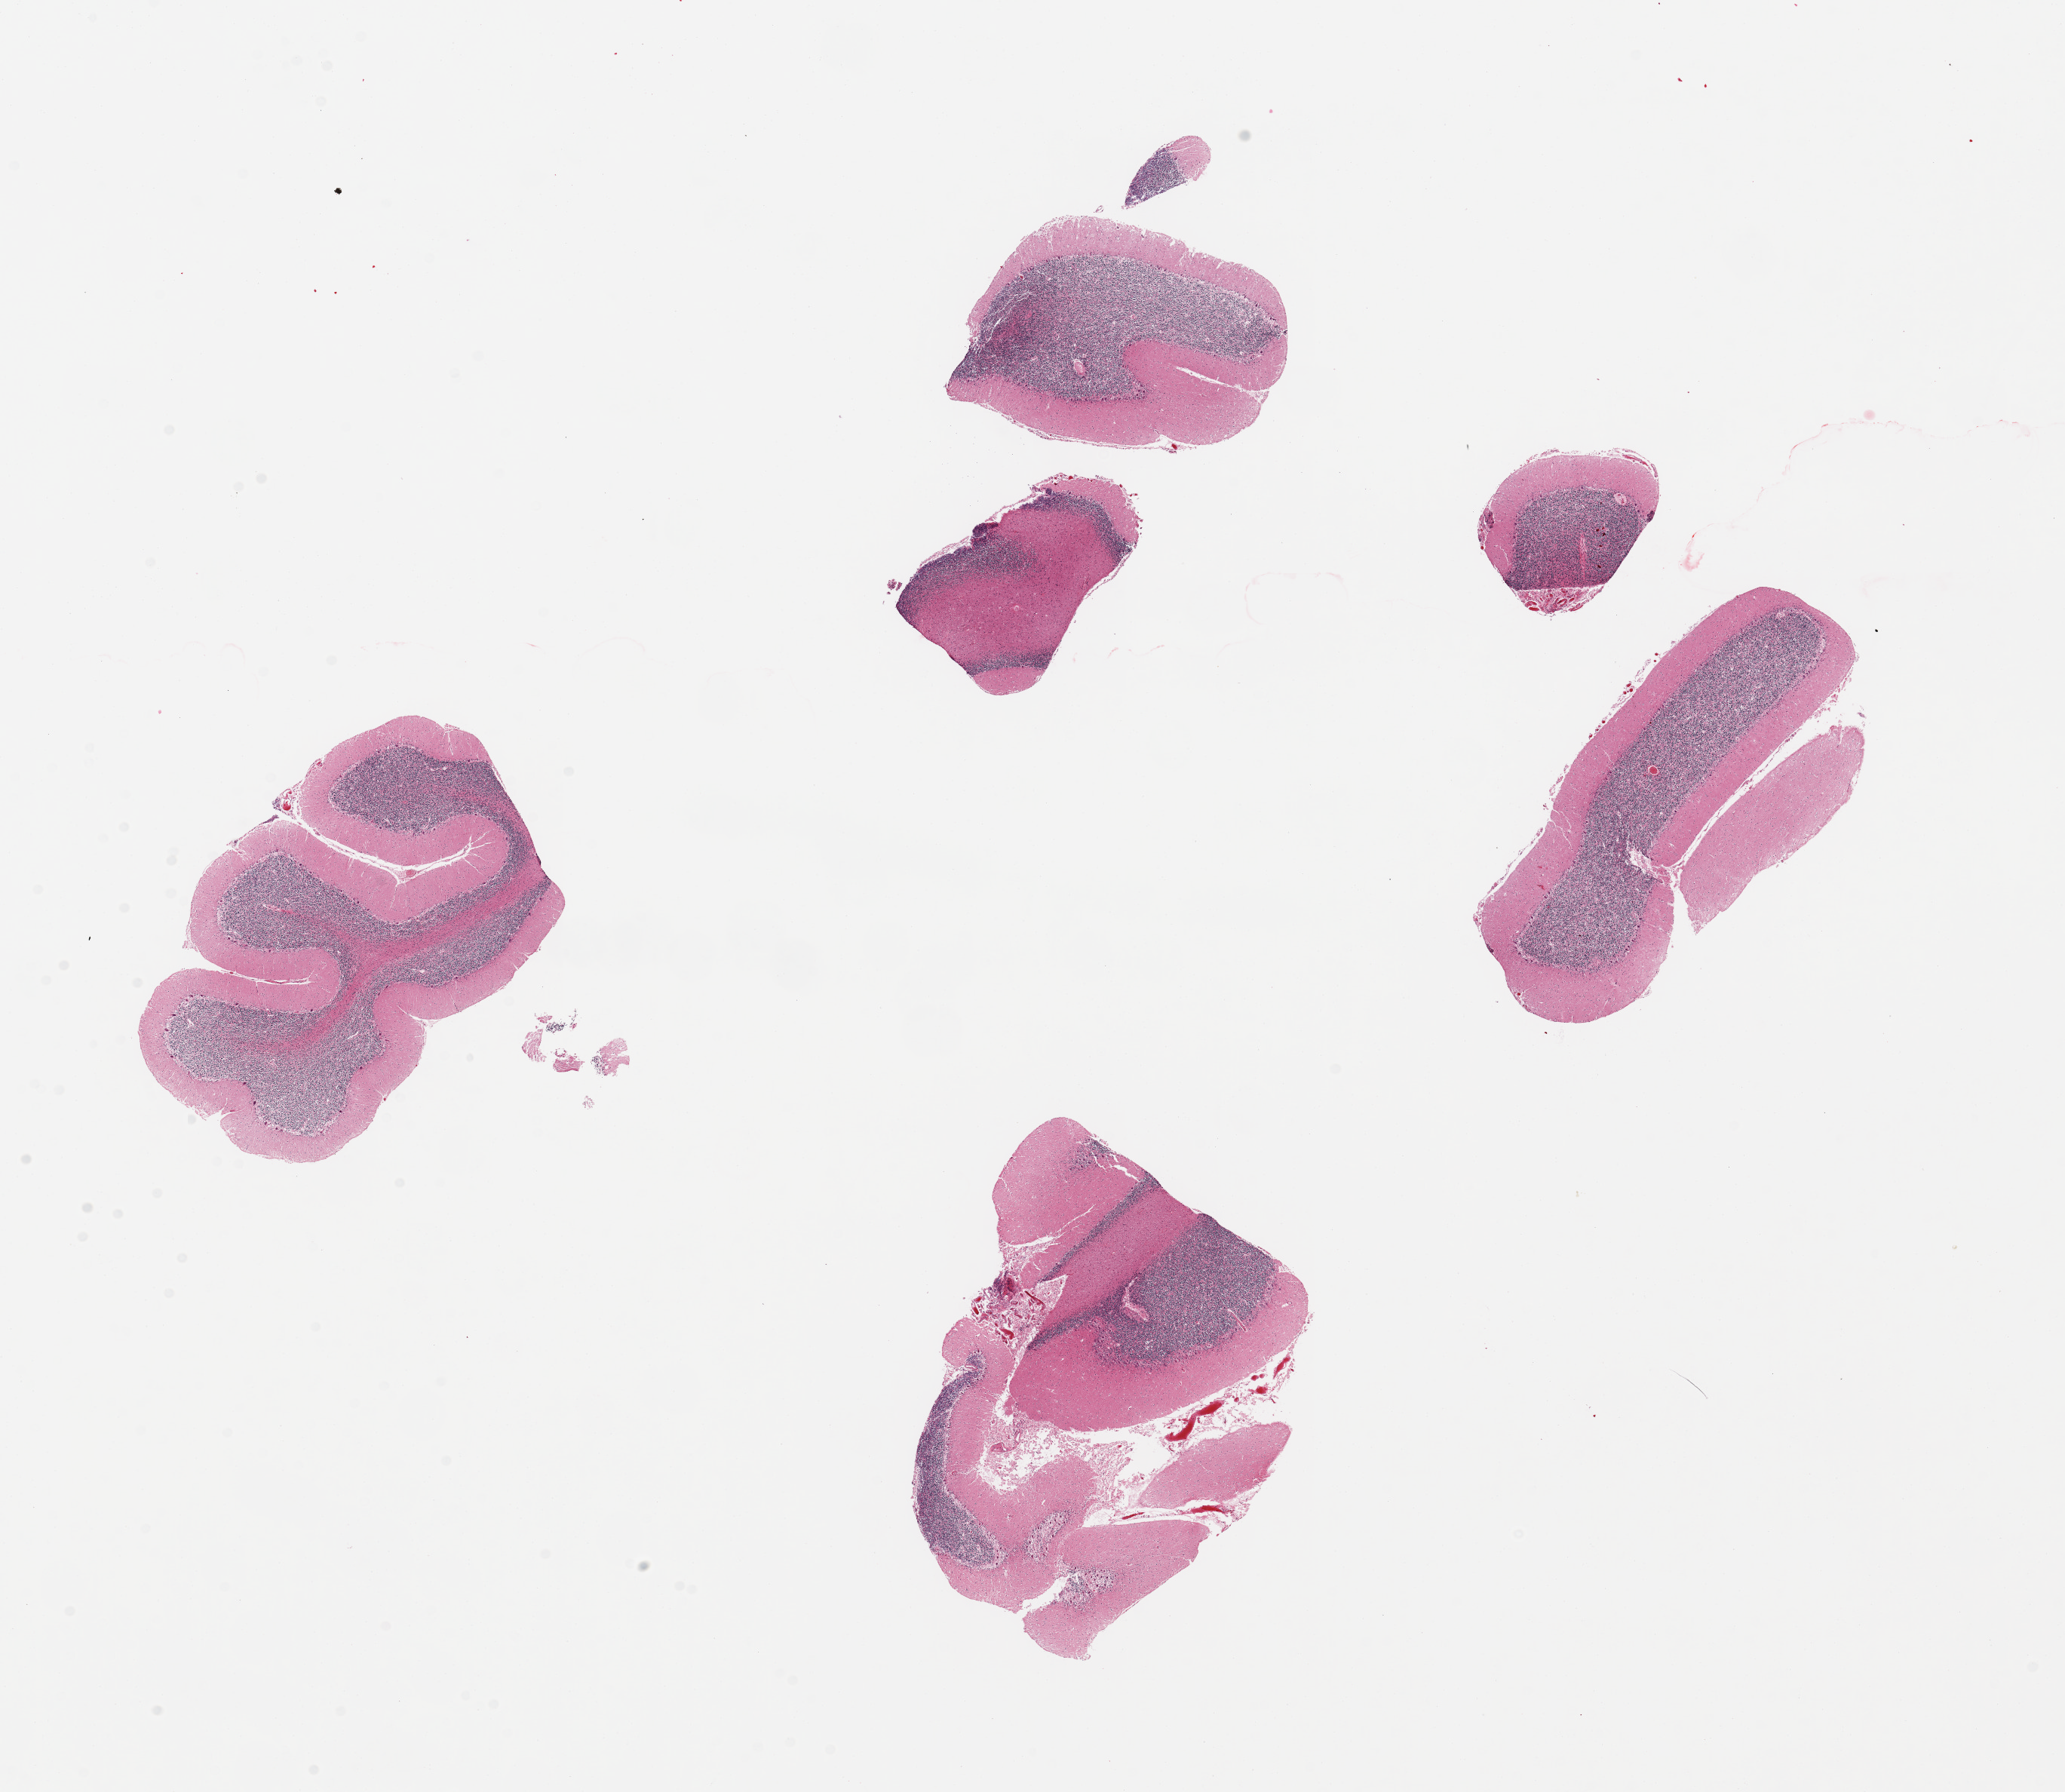
H&E whole-slide image, a low-resolution overview of the entire scanned area, about 21.7 x 18.8 mm. PAXgene-fixed, paraffin-embedded tissue. Target tissue: cerebellum. Tissue donor sample. Donor: female.
Pathologist's review note for this sample: 6-7 pieces (fragments) no abnormalities.